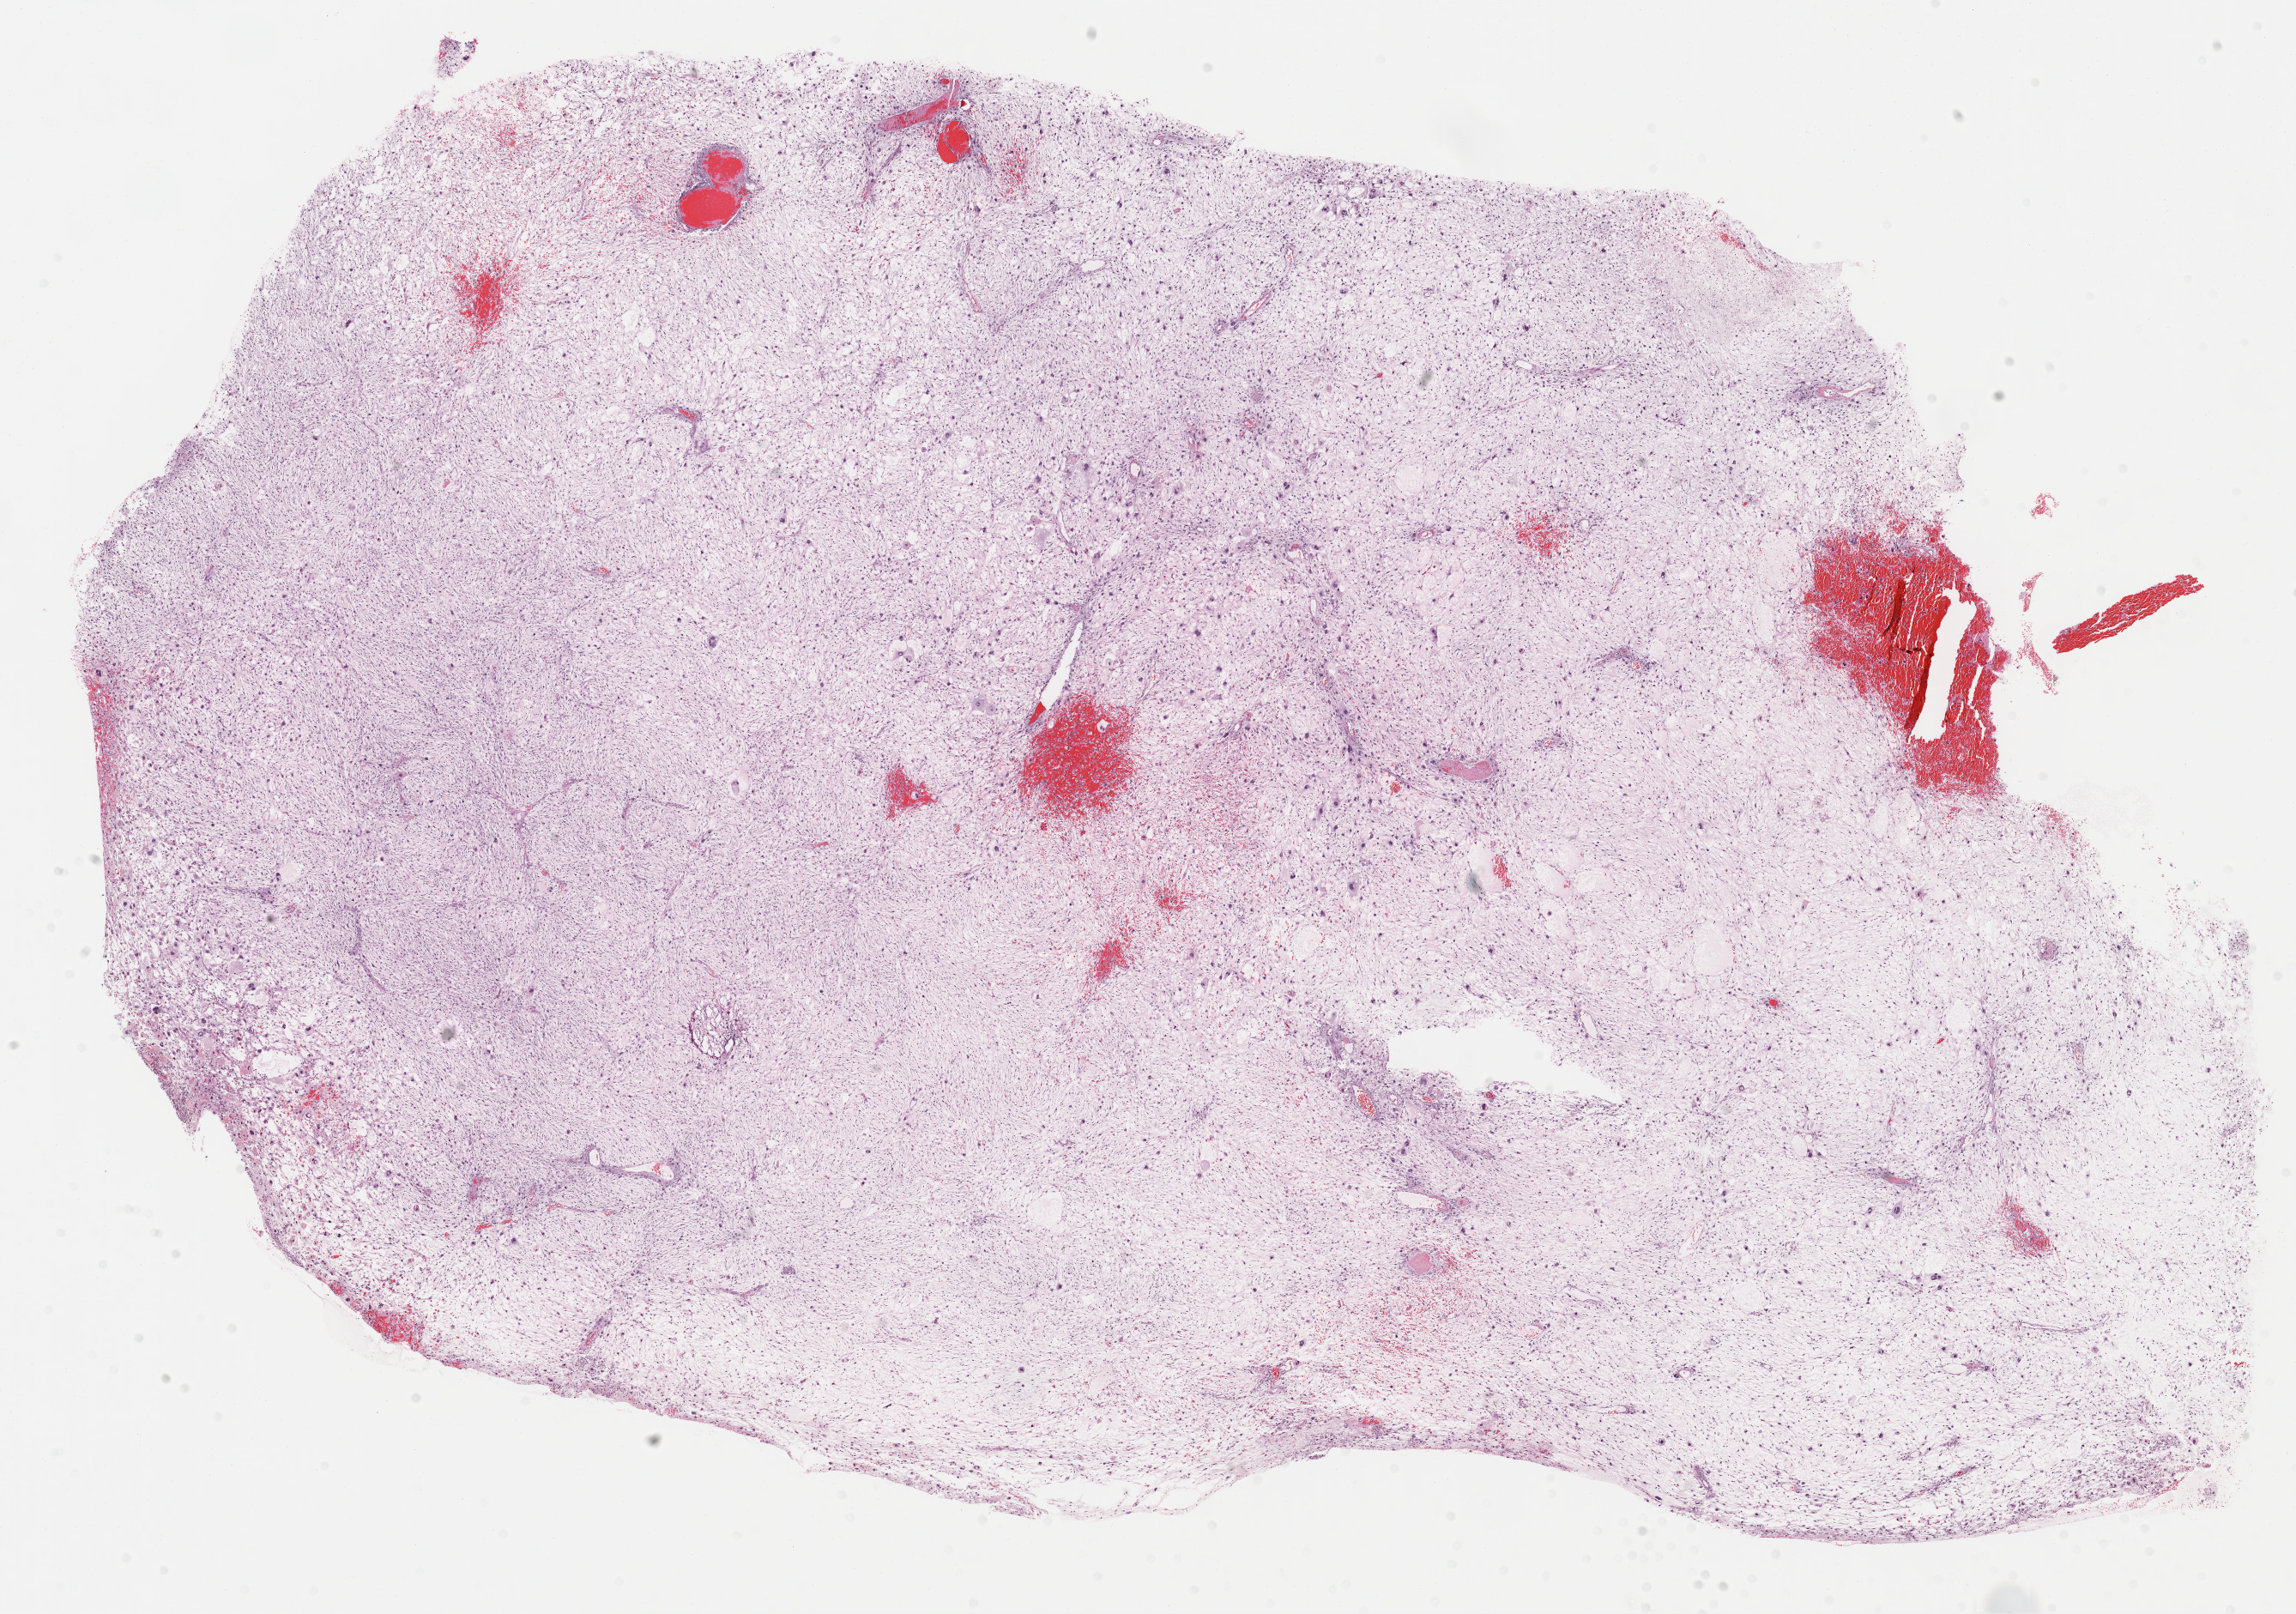
Digitized Hematoxylin and eosin (H&E) stained tissue section (whole slide), whole scanned area (about 21.6 x 15.2 mm) shown as a low-resolution overview, formalin-fixed paraffin-embedded (FFPE) diagnostic section, connective, subcutaneous and other soft tissues, primary tumour sample. Patient: male, age at initial diagnosis 74 years.
- diagnosis: Fibromyxosarcoma